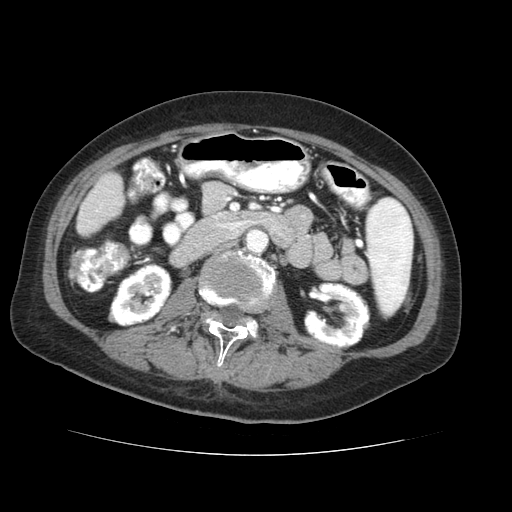
Contrast-enhanced abdominal CT (liver protocol), one axial slice. Position 6 of 73 along the scan axis. Reconstruction kernel STANDARD. 120 kVp. Soft-tissue window (W 400 / L 40 HU). 2.5 mm slice thickness. 512 × 512 image matrix, field of view 360 × 360 mm. Case-level facts recorded for this patient, not image findings: diagnosis: hepatocellular carcinoma (patient treated with transarterial chemoembolisation; whether this scan precedes or follows treatment is not stated here); TNM stage (as recorded): Stage-IVB; Child-Pugh class: A; tumour differentiation: well differentiated; tumour nodularity: uninodular.
Outlined on this slice (semi-automatic segmentation, software-assisted and operator-edited):
- liver parenchyma outside the tumour (the mass and vessels are separate outlines, so this box may not span the whole liver): bounding box <76,172,124,236> (left, top, right, bottom; pixels)
- liver vessels: <79,191,103,227>